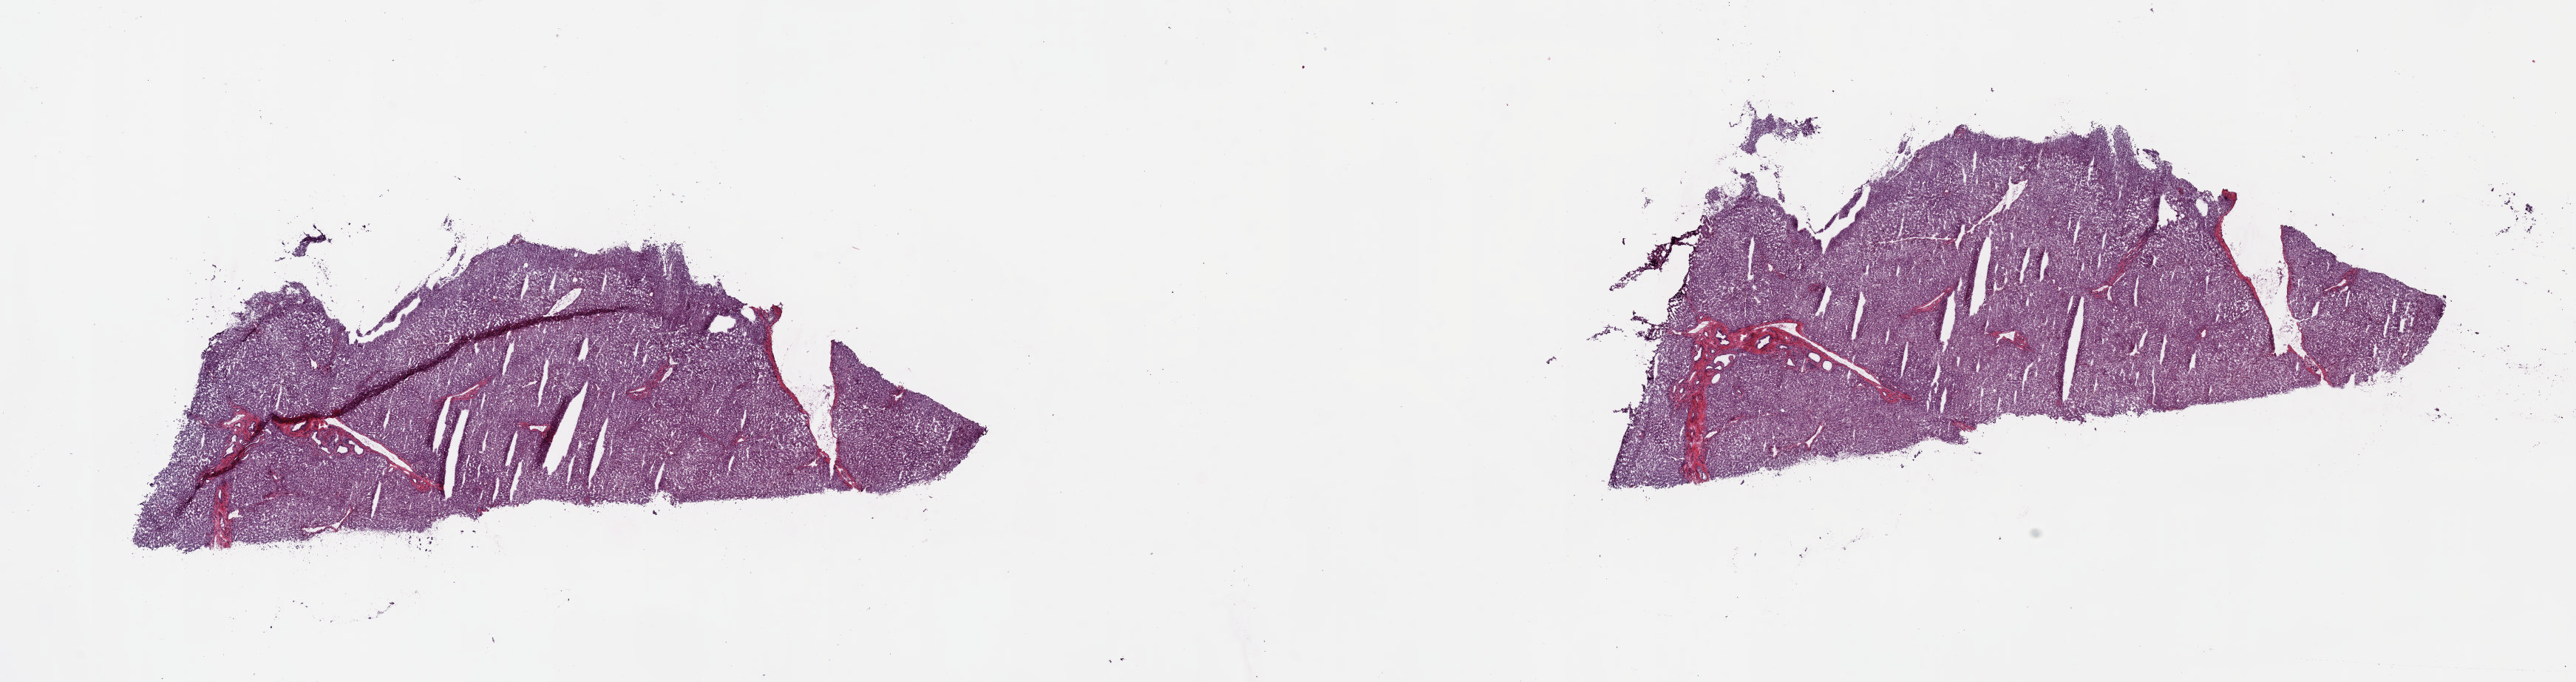
H&E whole-slide image — whole scanned area (about 27.5 x 7.3 mm, slide scanned at 20x) shown as a low-resolution overview. Frozen section from the top of the tissue portion. Sample: solid tissue normal (non-tumour tissue), liver. Male, age 46 years at initial diagnosis. Composition of this section per pathologist review: tumour cells 0%, tumour nuclei 0%, normal cells 100%, stromal cells 0%, necrosis 0%. Infiltration values recorded for this section: lymphocyte infiltration 1%, monocyte infiltration 0%, neutrophil infiltration 0%.
This section: solid tissue normal sample (biorepository sample class). Patient diagnosis: Hepatocellular carcinoma, NOS.